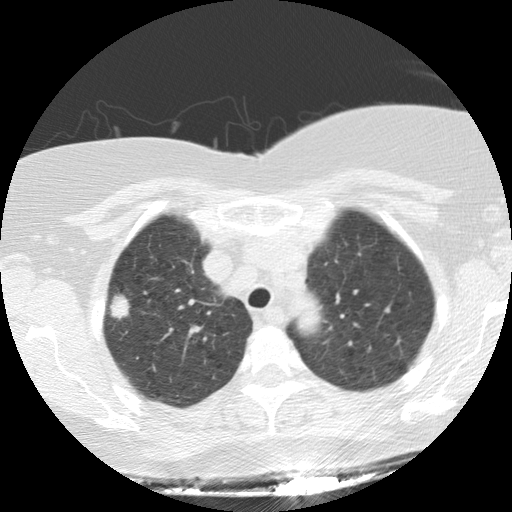
Low-dose screening chest CT, one axial slice. Position 110 of 136 along the scan axis. Reconstruction kernel STANDARD. Lung window (W 1500 / L -600 HU). 512 × 512 image matrix, field of view 330 × 330 mm.
Structures marked on this image (manually delineated by an expert):
- lesion 1 (tumor, upper lobe of right lung): bounding box <110,294,131,320> (left, top, right, bottom; pixels)